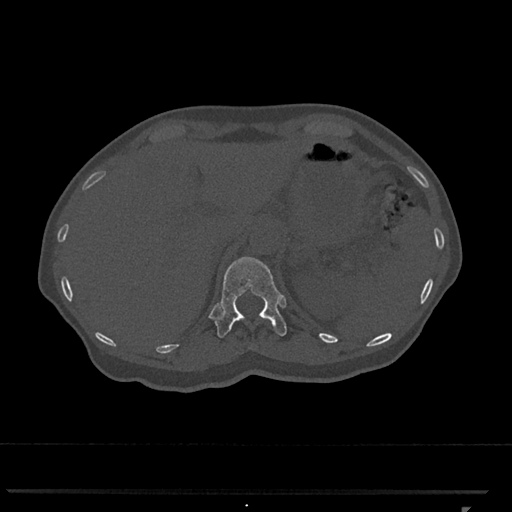
CT including the spine, one axial slice. Slice 473 of 793 in the series (ordered by position). Reconstruction kernel Br40s/3. 120 kVp. Bone window (W 1800 / L 400 HU). 512 × 512 image matrix. Female patient, age 62 years. Case-level facts recorded for this patient, not image findings: primary cancer: renal.
Structures marked on this image (semi-automatically segmented with operator editing):
- T12 vertebra: bounding box [x1, y1, x2, y2] px = [215, 256, 287, 338]